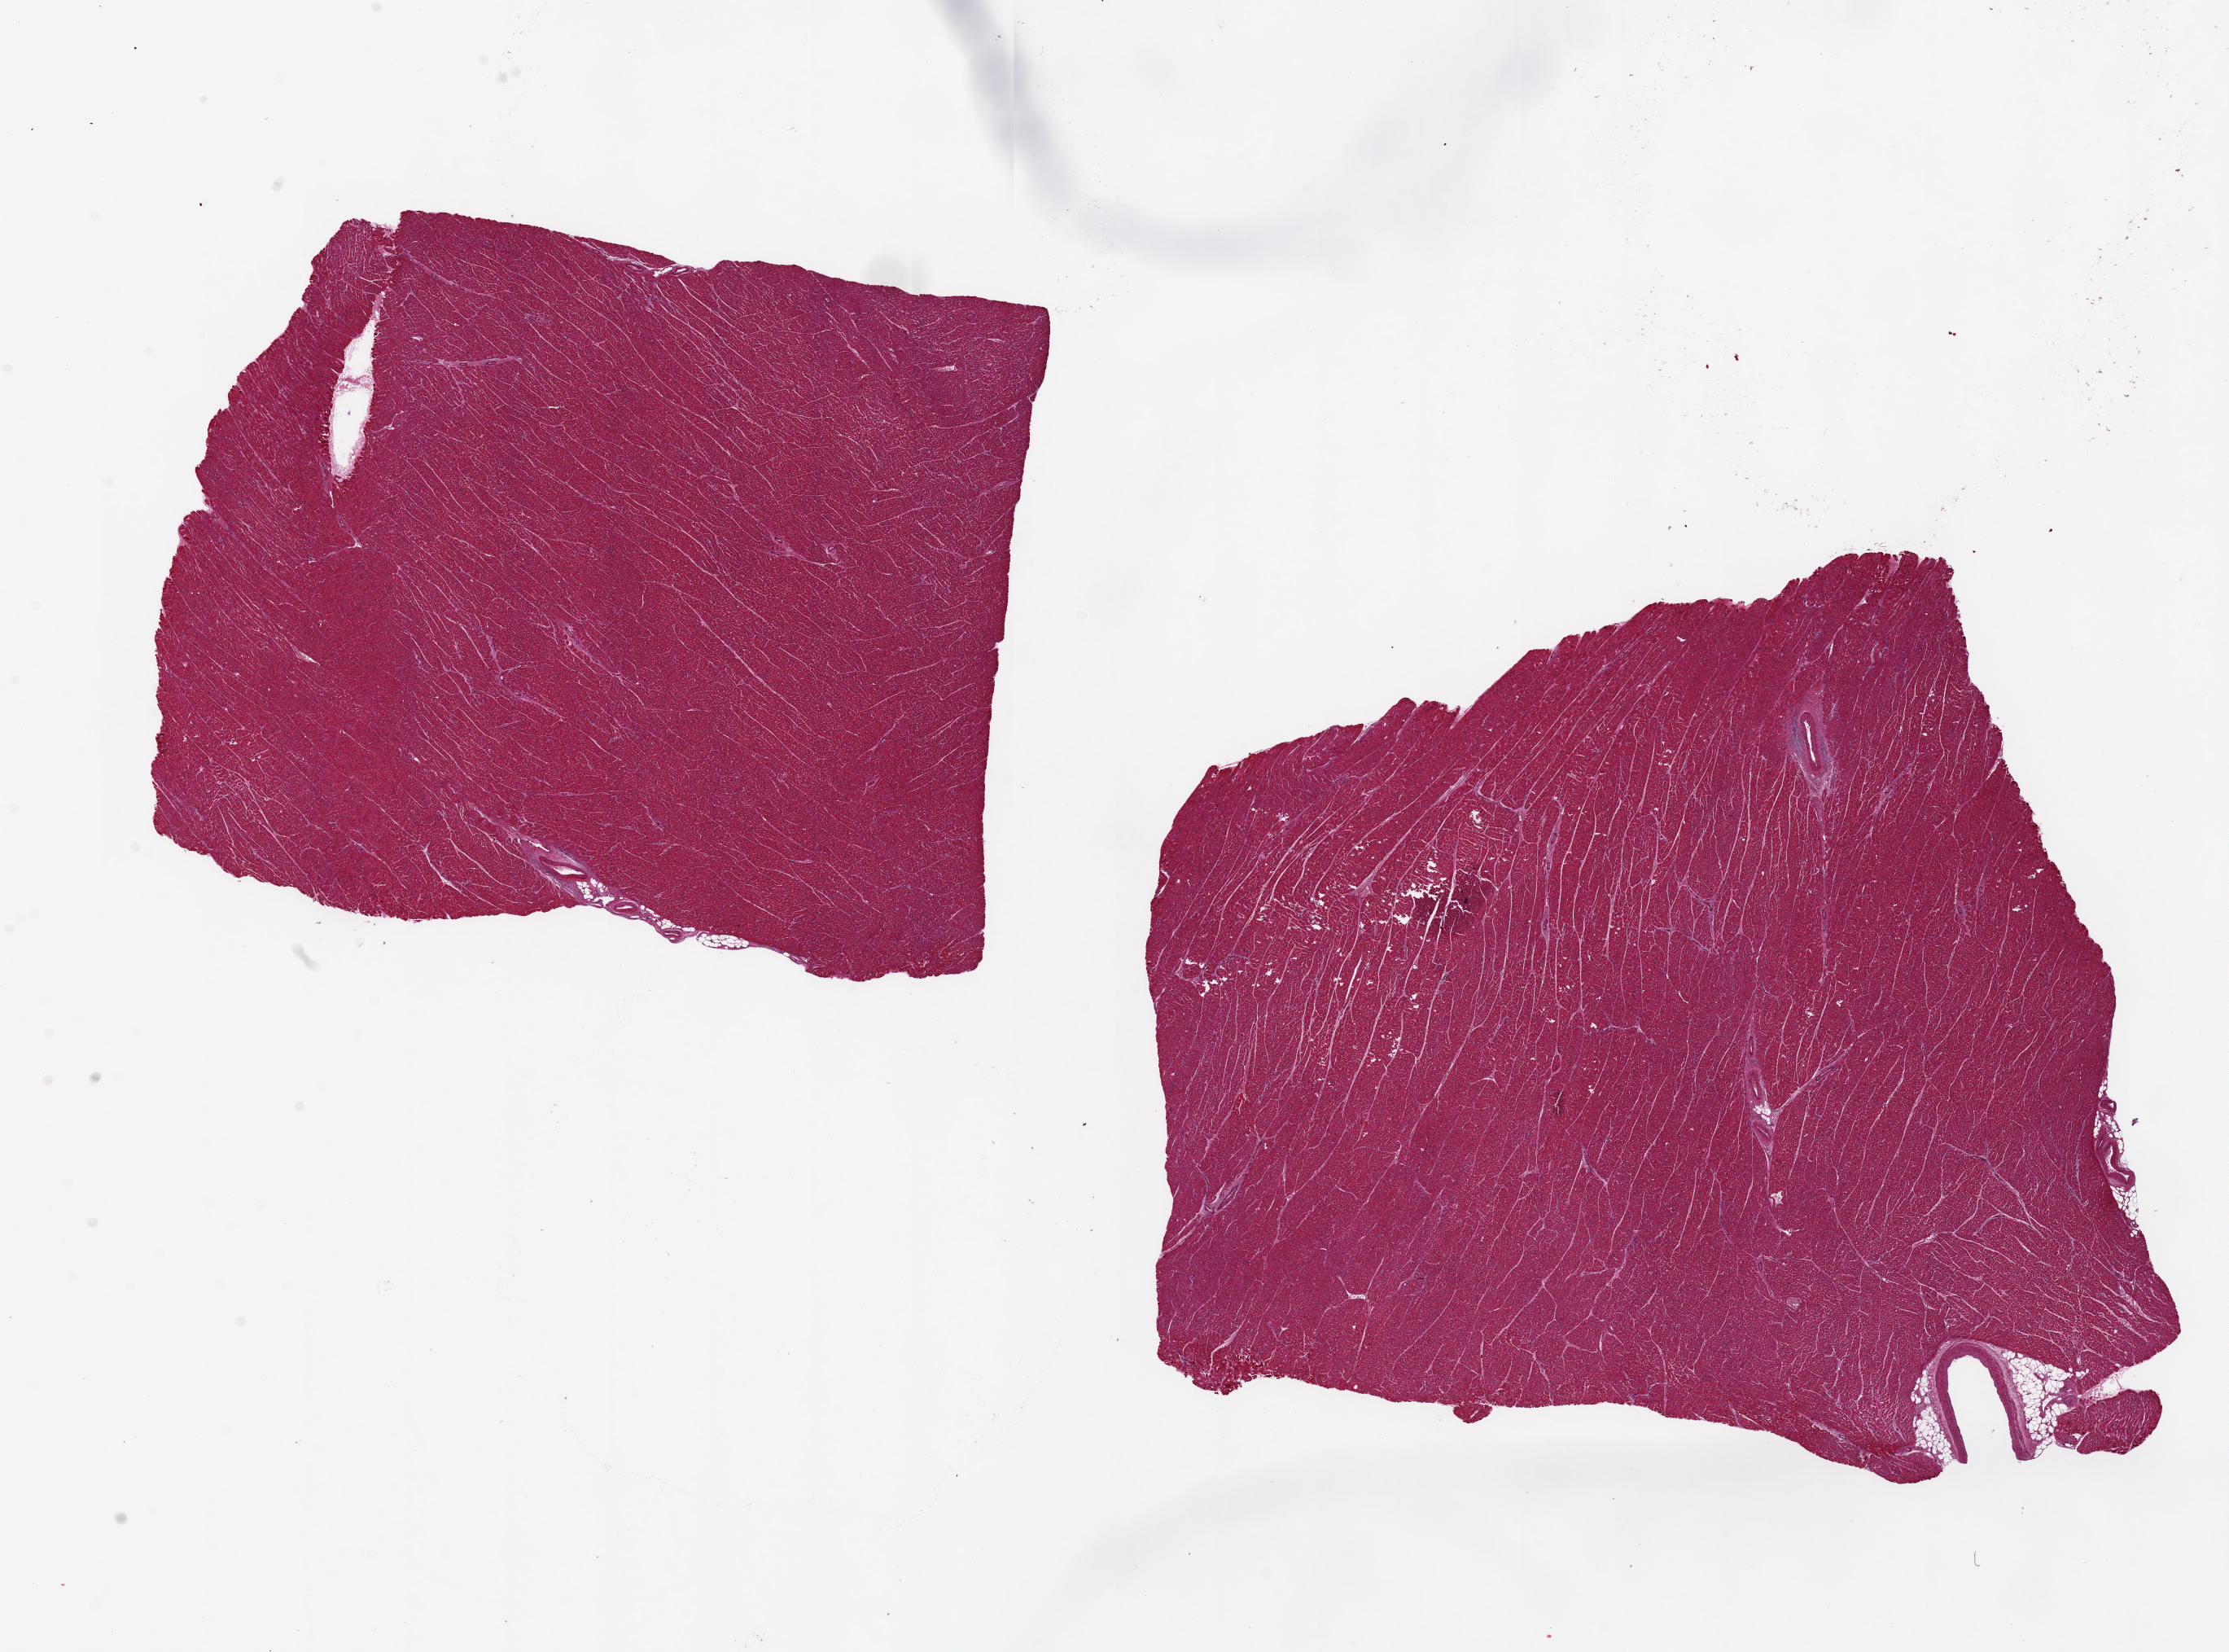
Whole-slide image, hematoxylin and eosin (H&E) stain, brightfield, whole scanned area (about 21.7 x 16.0 mm) shown as a low-resolution overview. PAXgene-fixed paraffin-embedded (PFPE) section. Sampled site (target tissue): heart. Tissue donor sample. Male donor.
* reviewer comment on this tissue sample: 2 pieces ~8x7mm, Minimal ischemic changes